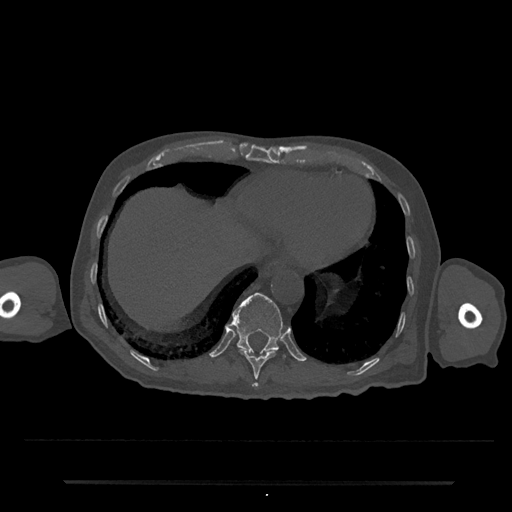
CT including the spine, one axial slice; position 284 of 797 along the scan axis; reconstruction kernel Br40s/3; 120 kVp; bone window (W 1800 / L 400 HU); 0.5 mm slice thickness; 512 × 512 image matrix, field of view 427 × 427 mm. Male patient, age 74 years. Case-level facts recorded for this patient, not image findings: primary cancer: prostate.
Annotated regions visible in this slice (semi-automatic segmentation, software-assisted and operator-edited):
- T10 vertebra: bounding box <239,349,277,387> (left, top, right, bottom; pixels)
- T11 vertebra: <230,292,285,357>